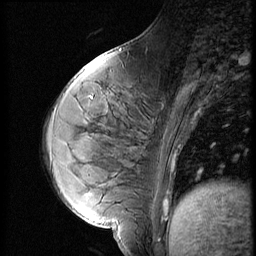
Breast MRI (dynamic contrast-enhanced), one sagittal slice. Slice 20 of 56 in the series (ordered by position). 3 images stored at this slice position (order not interpretable as contrast timing). 1.5 T. TE 4.2 ms, TR 9 ms. 2.5 mm slice thickness. 256 × 256 image matrix. Patient: female, 35 years. From the clinical record (not read from this slice): setting: breast cancer imaged before/during neoadjuvant chemotherapy; receptor status: HR-positive, HER2-negative.
Structures marked on this image (semi-automatic segmentation, software-assisted and operator-edited):
- analysis volume of interest (the breast-tissue region the enhancement analysis was run in; not a lesion): box from (x=58, y=70) to (x=171, y=208) px
- tumour enhancement mask (voxels above the 140 % enhancement threshold inside the analysis volume of interest): (x=163, y=201)–(x=168, y=208)